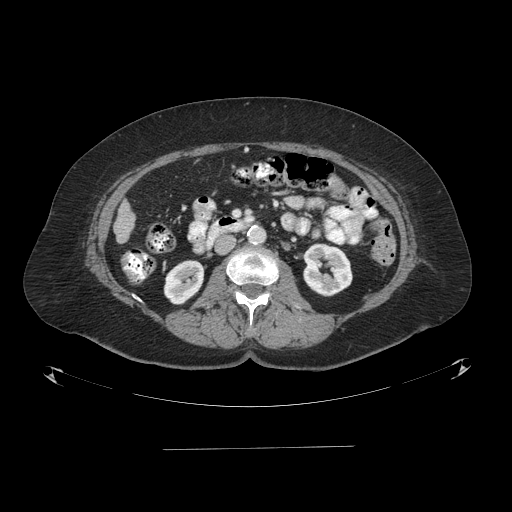
Contrast-enhanced abdominal CT (liver protocol), one axial slice; slice 18 of 103 in the series (ordered by position); one of 2 acquisitions stored at this slice position; soft-tissue window (W 400 / L 40 HU); 2.5 mm slice thickness; 512 × 512 image matrix. From the clinical record (not read from this slice): diagnosis: hepatocellular carcinoma (patient treated with transarterial chemoembolisation; whether this scan precedes or follows treatment is not stated here); TNM stage (as recorded): Stage-IIIA; Child-Pugh class: A; tumour differentiation: poorly differentiated; tumour nodularity: multinodular.
Outlined on this slice (semi-automatic segmentation, software-assisted and operator-edited):
- liver parenchyma outside the tumour (the mass and vessels are separate outlines, so this box may not span the whole liver): bounding box <114,201,134,242> (left, top, right, bottom; pixels)